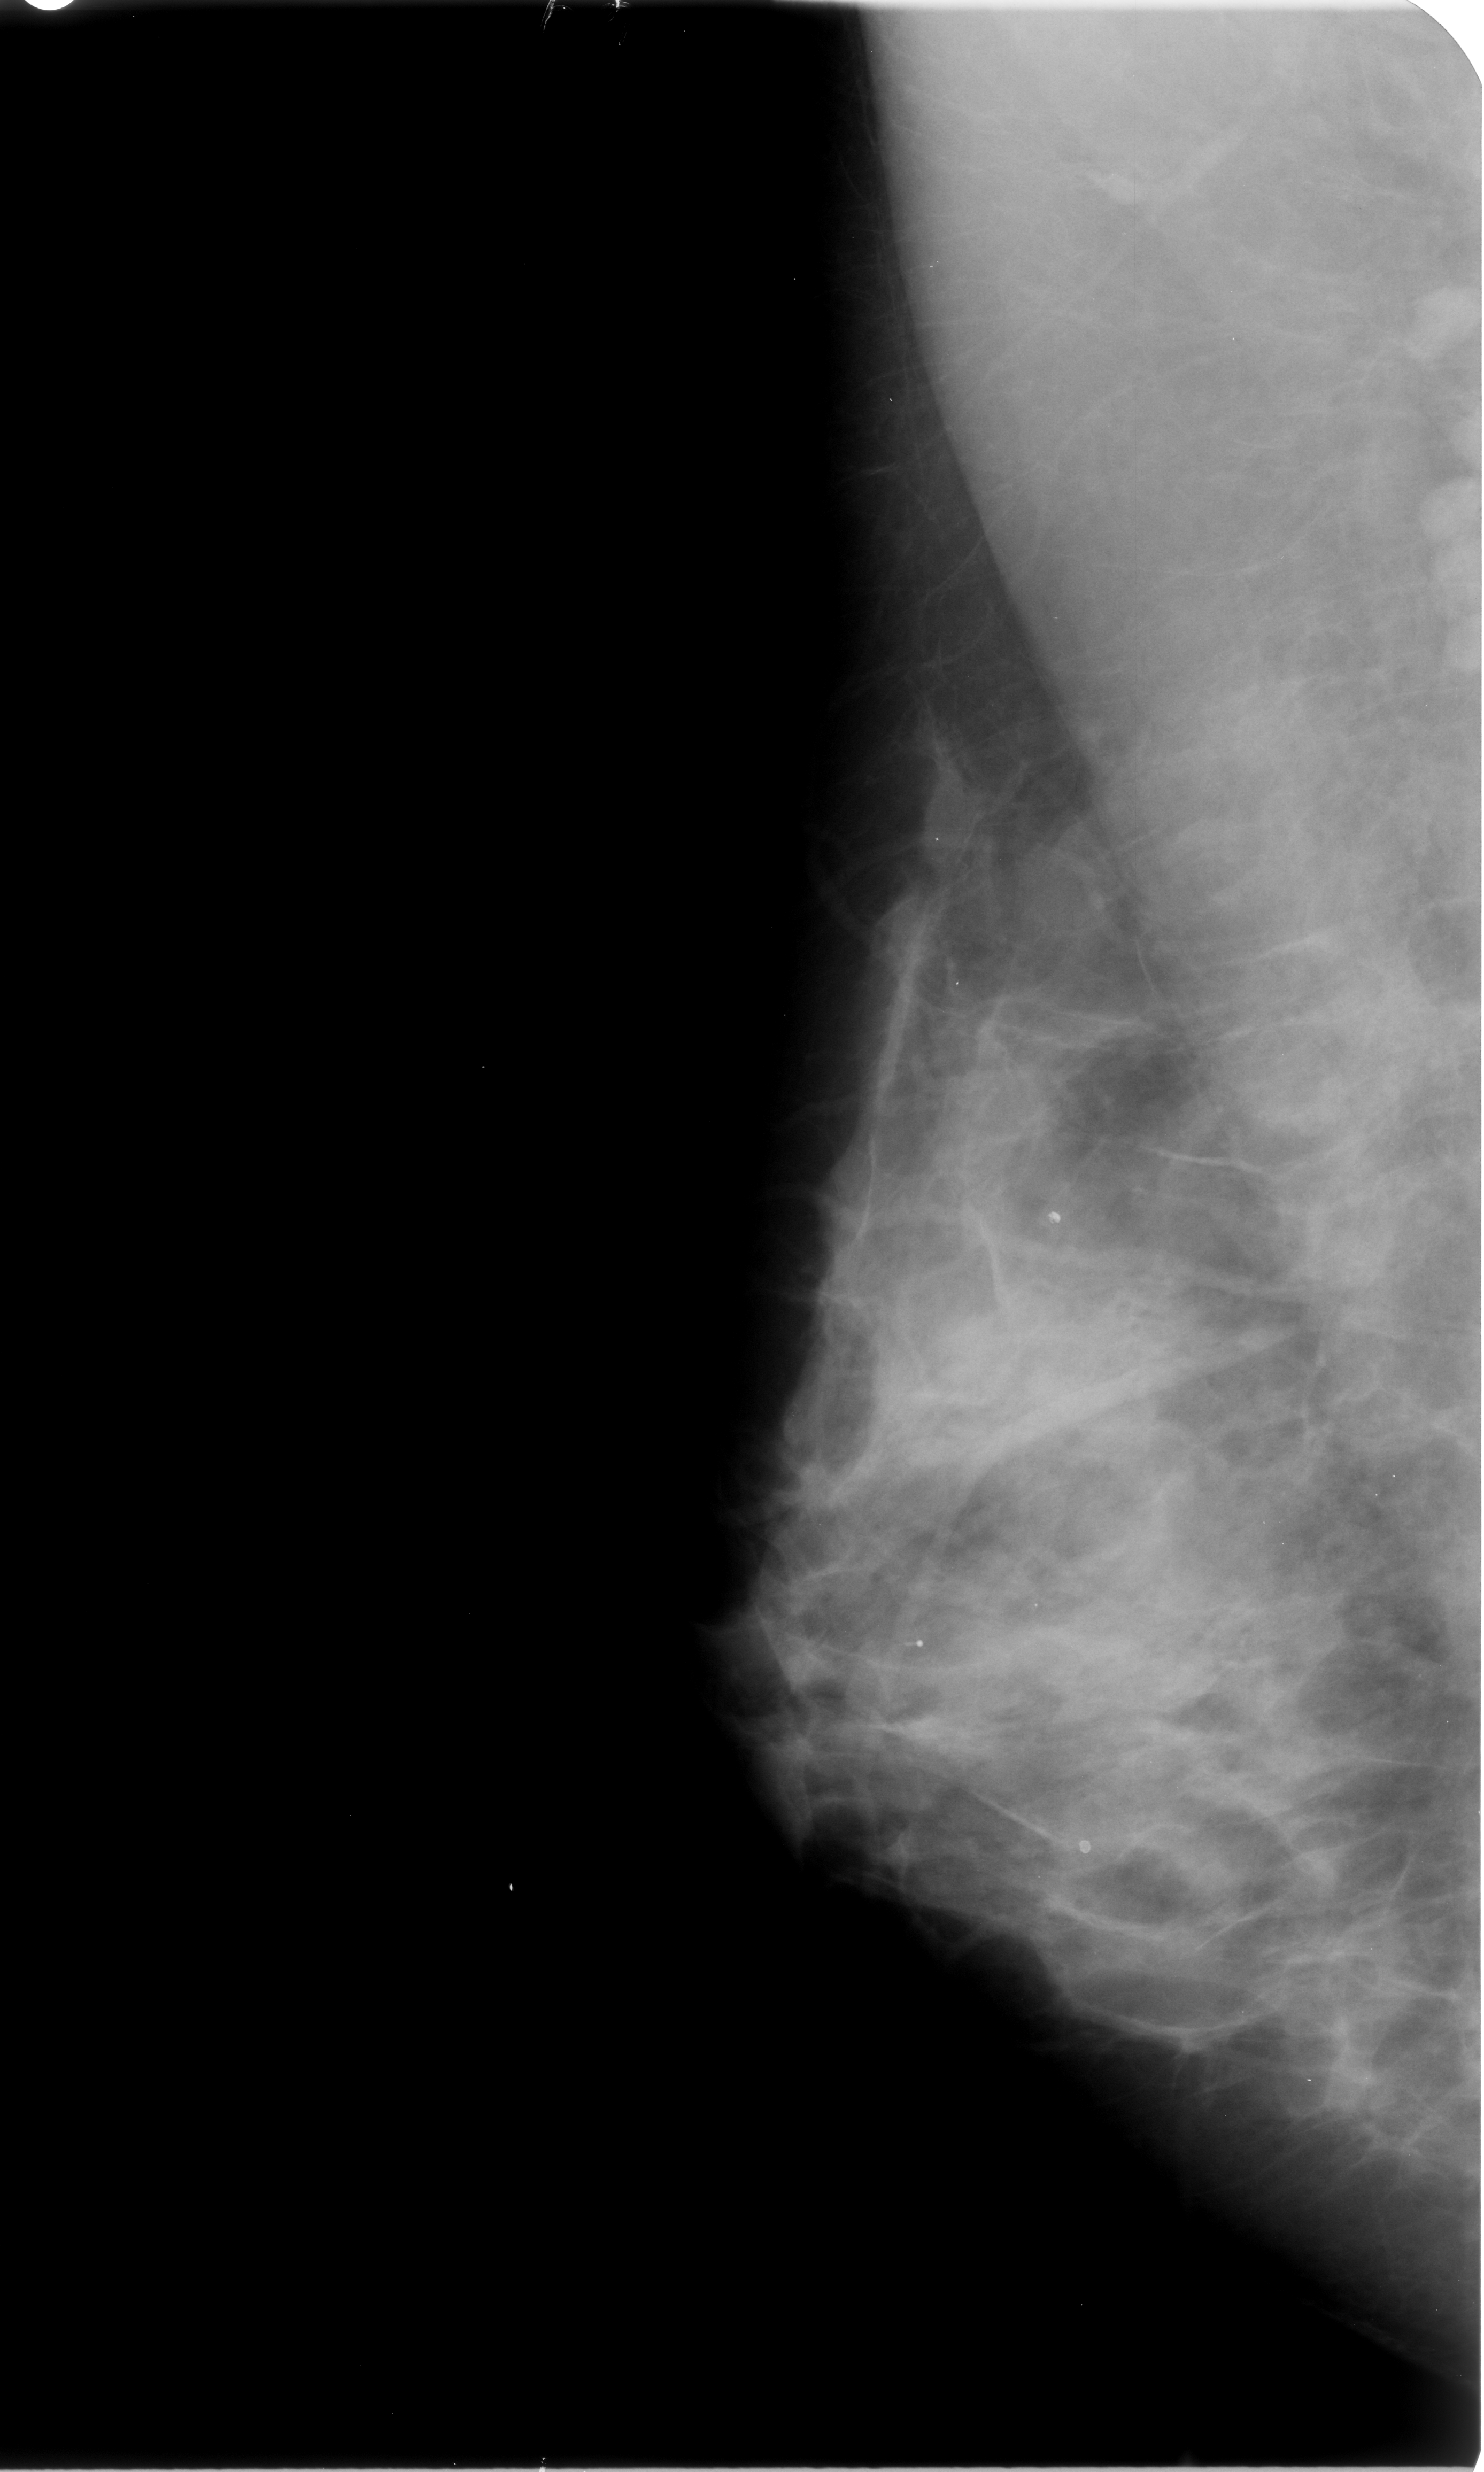
Scanned film-screen mammogram, right breast, MLO view, BI-RADS breast density category 3 (scale 1–4).
- Marked findings (only marked abnormalities are described; nothing is implied about the rest of the image): Finding 1 of 3: calcifications, morphology round and regular / lucent centered; BI-RADS assessment category 2; benign without callback (not worked up further).
- Finding 2 of 3: calcifications, morphology round and regular / lucent centered; BI-RADS assessment category 2; subtlety rating 3 on a 1 (subtle) to 5 (obvious) scale; benign without callback (not worked up further).
- Finding 3 of 3: calcifications, morphology round and regular / lucent centered; BI-RADS assessment category 2; benign; no additional work-up was recommended (benign without callback).